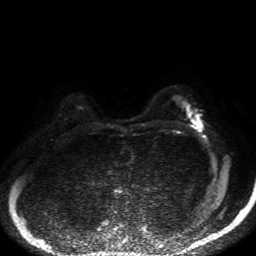
Breast MRI, one axial slice. Position 35 of 50 along the scan axis. Diffusion-weighted series; image 2 of 4 stored at this slice position (different b-values; order by instance number). 1.5 T. 4 mm slice thickness. 256 × 256 image matrix, field of view 320 × 320 mm. Female patient.
Structures marked on this image (expert manual segmentation):
- tumour on diffusion-weighted imaging: box from (x=194, y=120) to (x=201, y=125) px